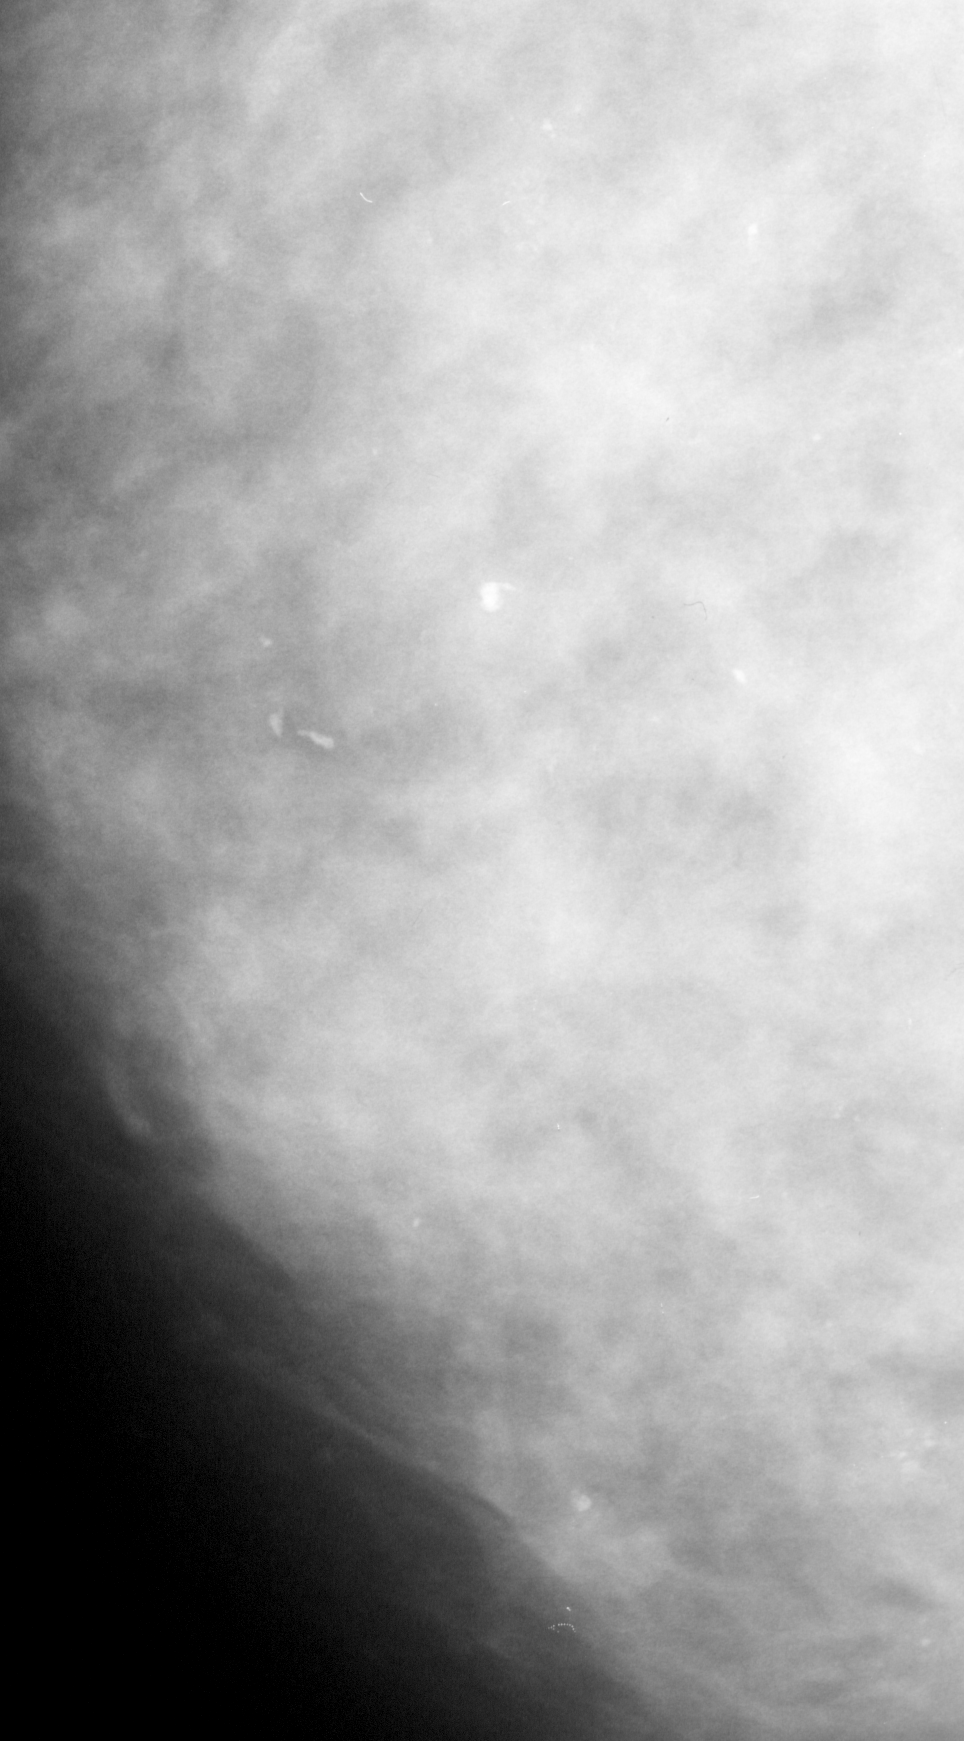
Cropped region of a digitized screen-film mammogram centred on a radiologist-marked abnormality, left breast, CC view, BI-RADS breast density category 3 (scale 1–4).
- Calcifications, morphology pleomorphic, distribution segmental; BI-RADS assessment category 4; pathology result (as recorded, not read from the image): malignant.